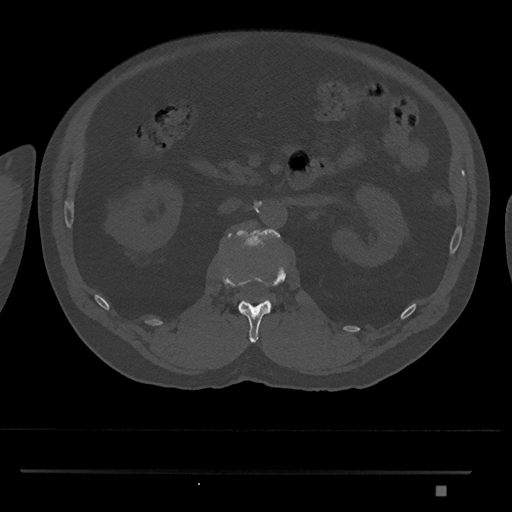
CT including the spine, one axial slice; slice 798 of 1134 in the series (ordered by position); reconstruction kernel Br40s/3; 120 kVp; bone window (W 1800 / L 400 HU); 512 × 512 image matrix. Male patient, age 65 years. Case-level facts recorded for this patient, not image findings: primary cancer: prostate.
Outlined on this slice (semi-automatically segmented with operator editing):
- L1 vertebra: bounding box [x1, y1, x2, y2] px = [223, 265, 286, 343]
- L2 vertebra: [227, 228, 281, 301]